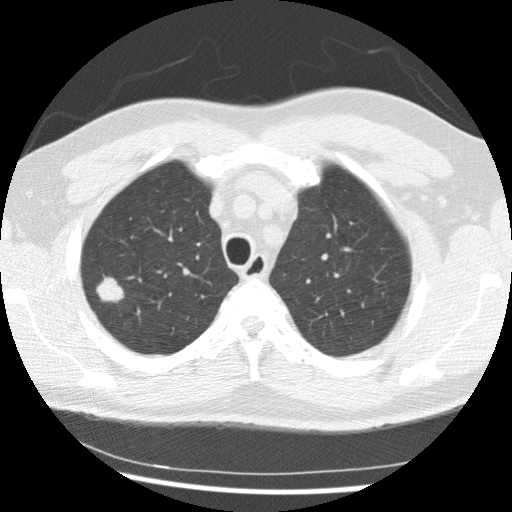
Low-dose screening chest CT, axial slice, first (baseline) screen, lung window (W 1500 / L -600 HU), standard (soft-tissue) reconstruction kernel (STANDARD), 120 kVp, 512 × 512 image matrix. Male participant, aged 56 years at enrolment. Current smoker at enrolment.
• Lesion marked by an expert reader, bounding box <79,270,131,315> (left, top, right, bottom; pixels).
• Reader record for this screening exam (exam-level; its link to the box is not recorded): non-calcified nodule or mass ≥4 mm, right upper lobe, 19 × 15 mm, spiculated (stellate) margins, soft tissue attenuation.
• Official screen result: positive, change unspecified: nodule(s) >= 4 mm or enlarging nodule(s), mass(es), or other non-specific abnormalities suspicious for lung cancer.
• Participant outcome: lung cancer diagnosed 291 days after this screen — non-small cell carcinoma, right upper lobe, poorly differentiated (G3), stage IIIB (AJCC 6th edition), 20 mm at pathology.